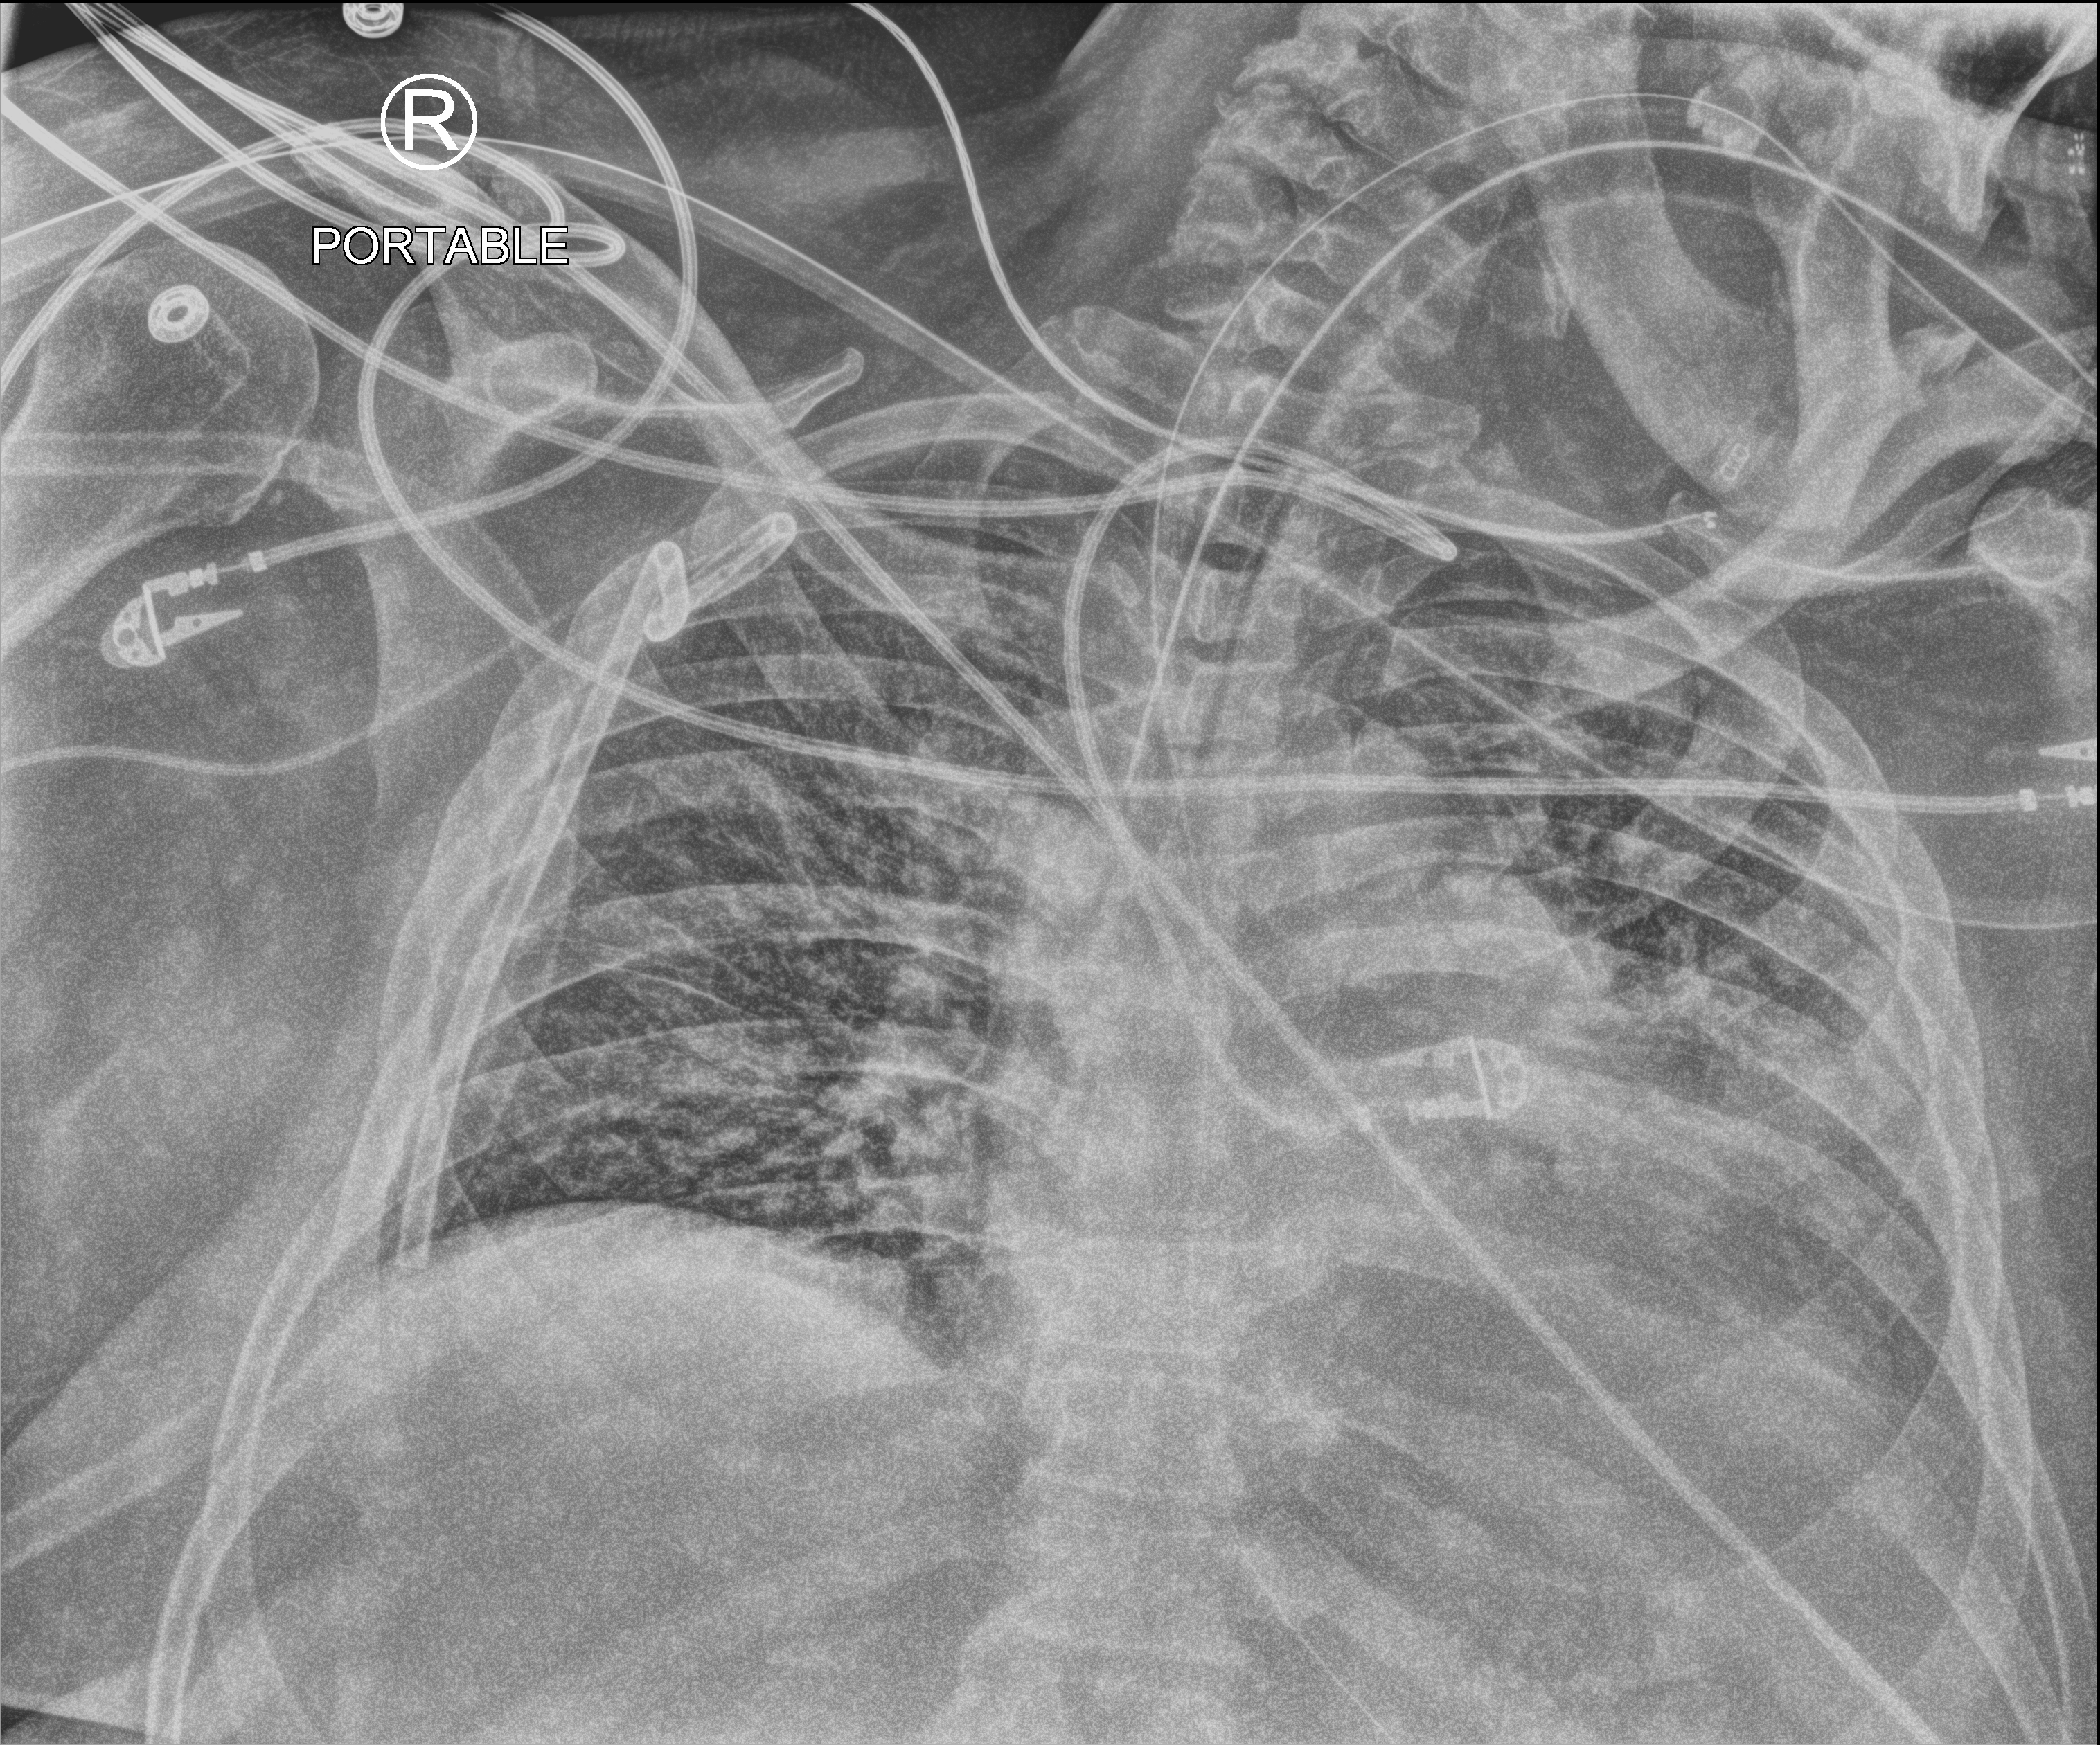
Chest X-ray (portable); anteroposterior (AP) projection. Male patient hospitalised with COVID-19, age 60–74 years.
Admission-level facts for this patient (not findings on this image; timing relative to this image not recorded):
- other chronic lung disease (admission record): no
- chronic kidney disease (admission record): no
- mechanically ventilated during this hospital stay: yes